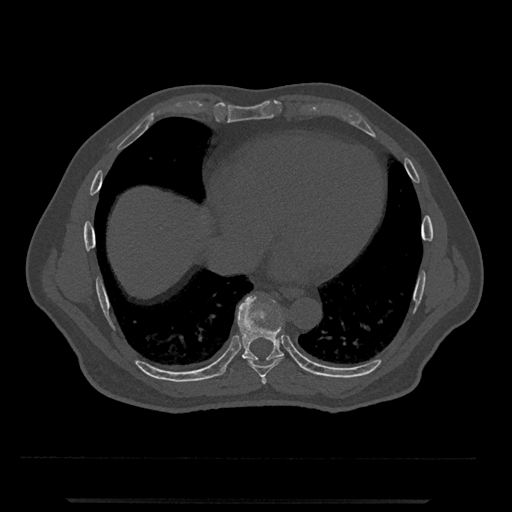
CT including the spine, one axial slice; position 600 of 797 along the scan axis; 120 kVp; bone window (W 1800 / L 400 HU); 512 × 512 image matrix. Male patient, age 63 years. Case-level facts recorded for this patient, not image findings: primary cancer: prostate.
Structures marked on this image (semi-automatically segmented with operator editing):
- T7 vertebra: bounding box [x1, y1, x2, y2] px = [261, 375, 267, 384]
- T8 vertebra: [248, 358, 283, 377]
- T9 vertebra: [221, 295, 284, 375]